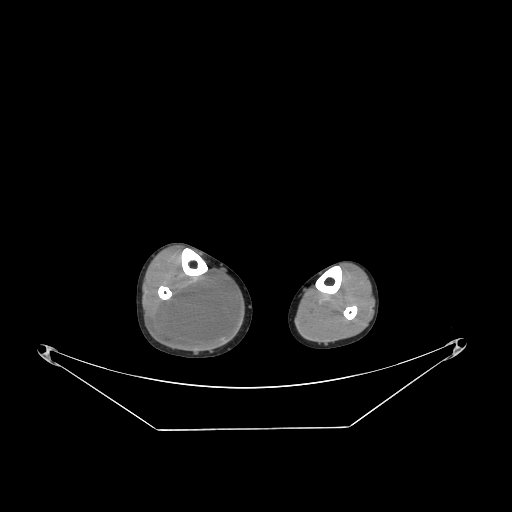
CT of an extremity soft-tissue mass (from a PET/CT study), one axial slice. Slice 92 of 267 in the series (ordered by position). 140 kVp. Soft-tissue window (W 400 / L 40 HU). 3.75 mm slice thickness. 512 × 512 image matrix, field of view 500 × 500 mm. Male patient. Case-level facts recorded for this patient, not image findings: histological type: liposarcoma - round cell; grade: high; site of the primary tumour: right calf.
Annotated regions visible in this slice (expert contour drawn on MRI and transferred to this co-registered scan by the dataset authors):
- gross tumour volume (mass): box from (x=153, y=272) to (x=239, y=350) px